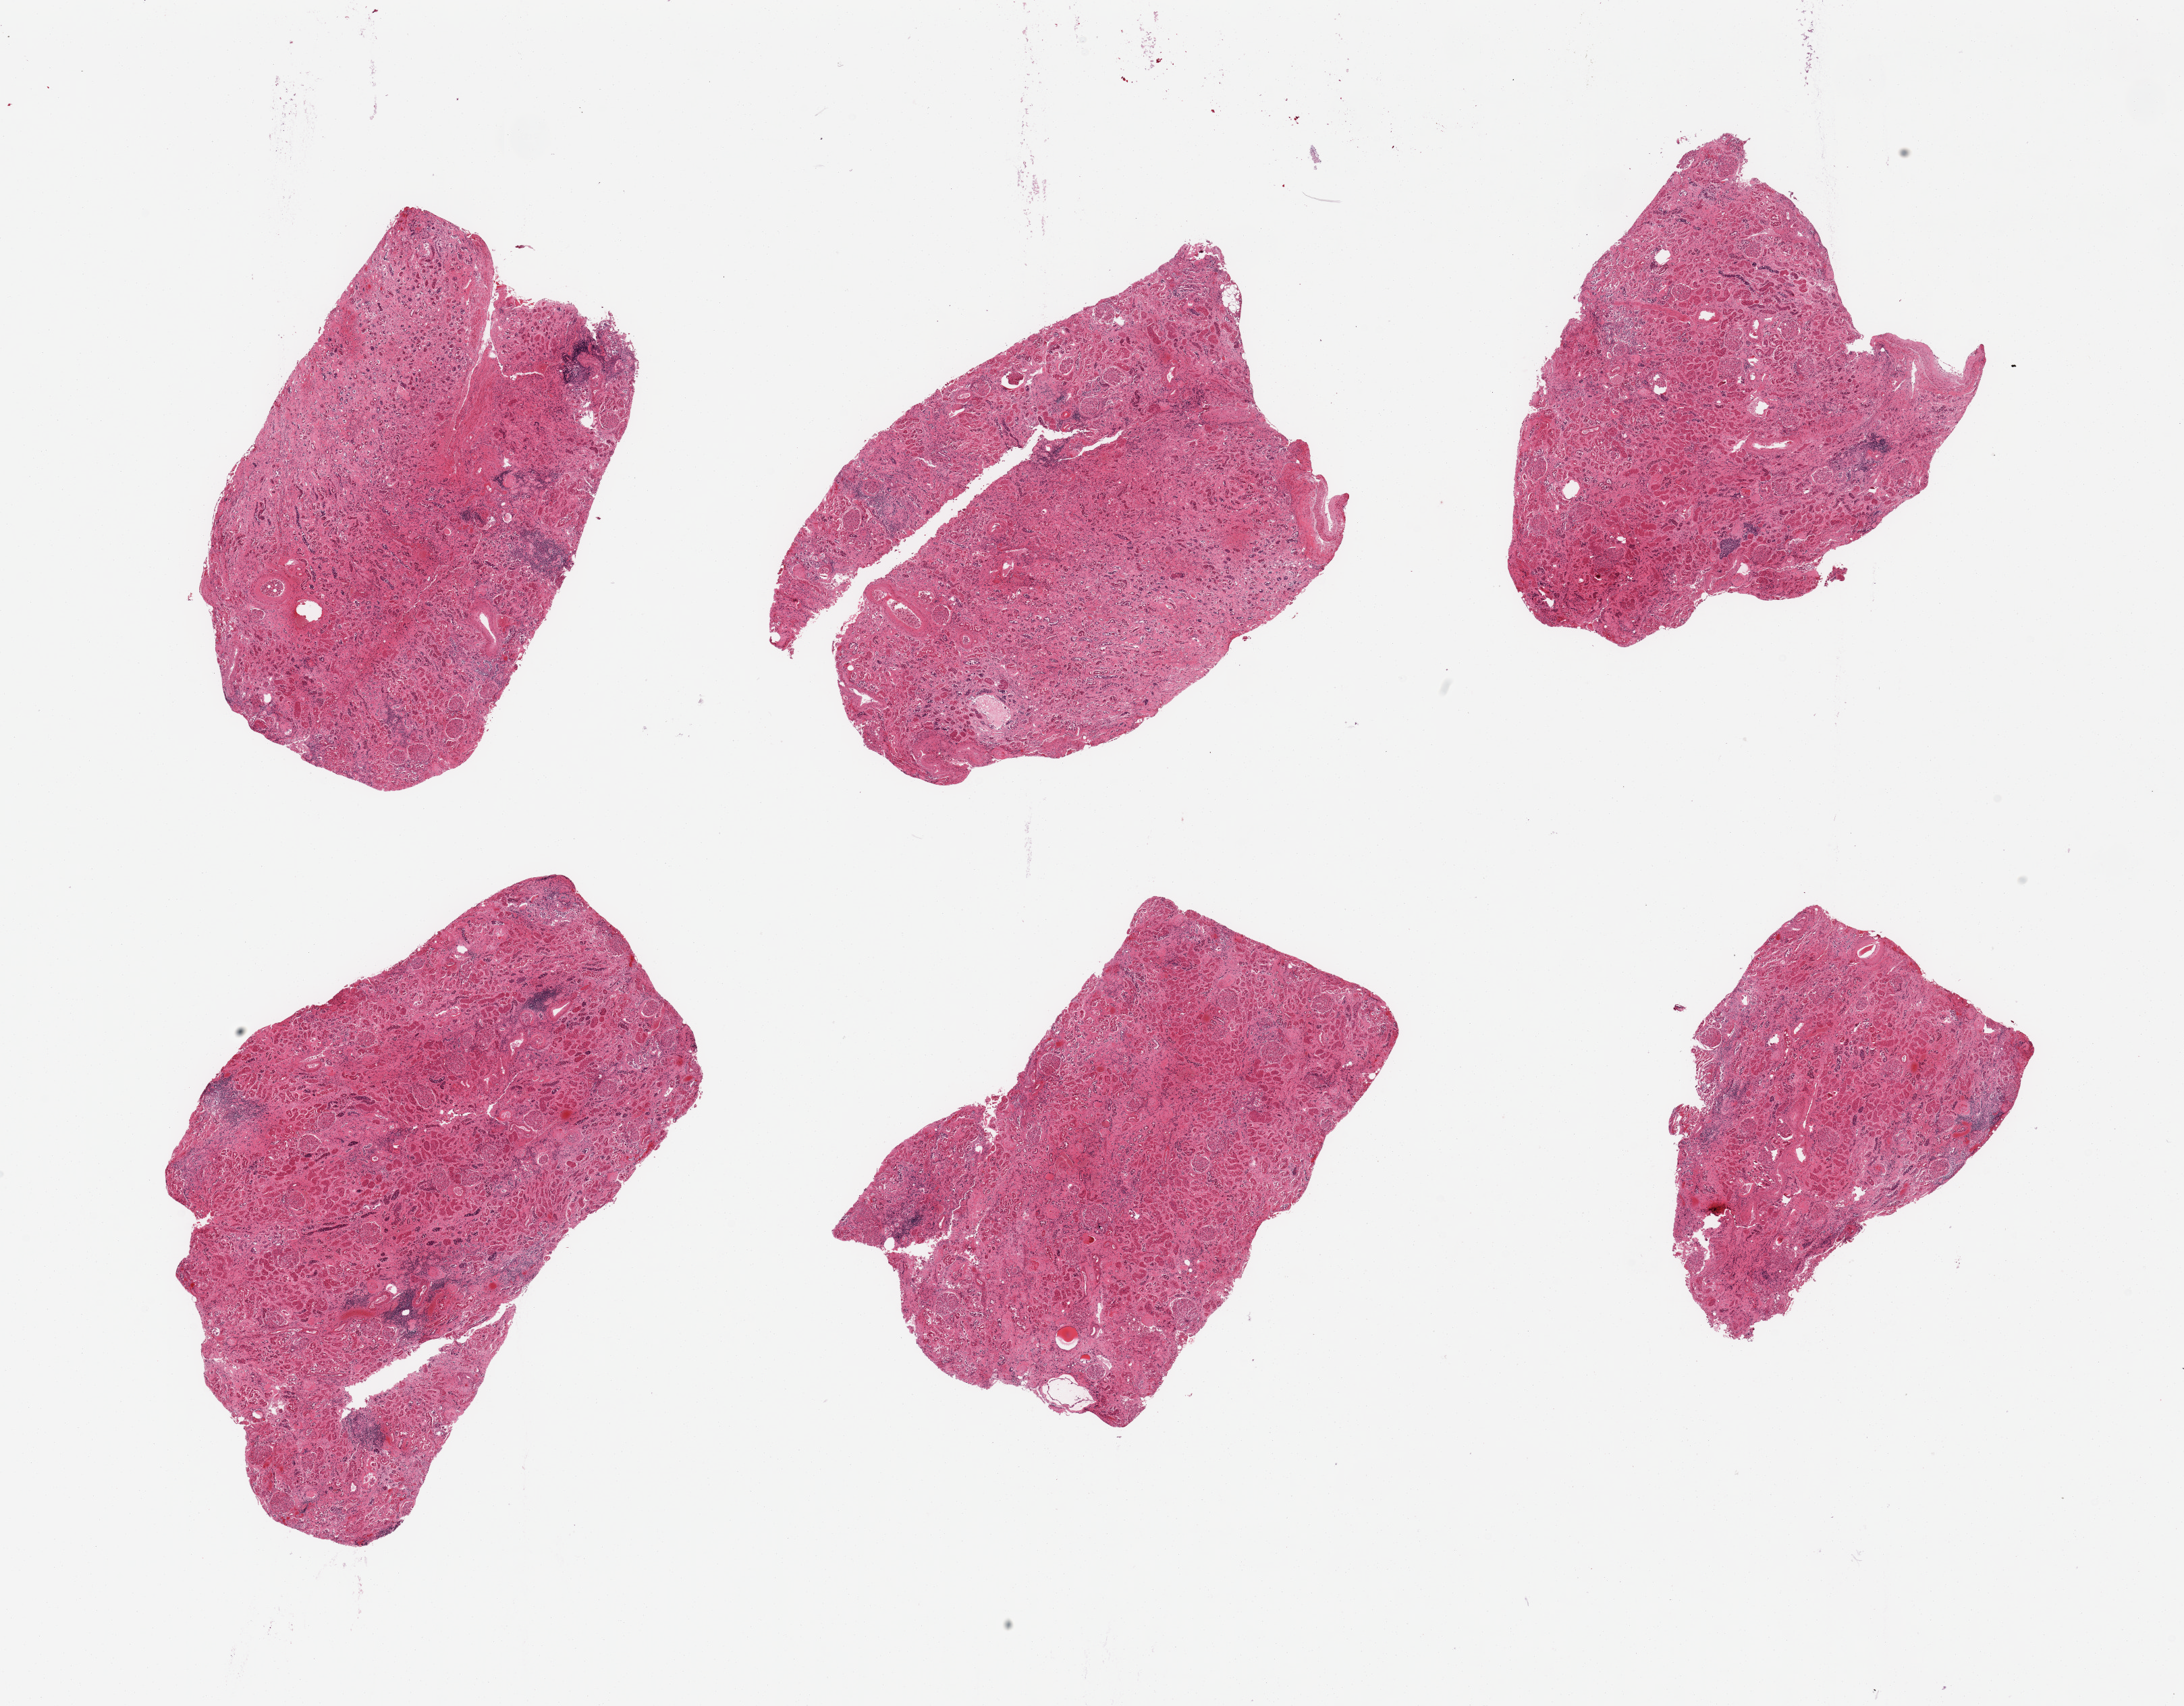
Digitized H&E-stained section — a low-resolution overview of the entire scanned area, about 25.6 x 20.0 mm (from a 20x scan). PAXgene-fixed, paraffin-embedded tissue. Target tissue: renal cortex. Donor tissue sample. Male donor.
Pathologist's review note for this sample: 6 pieces; tubules extensively autolyzed; glomeruli in somewhat better shape.